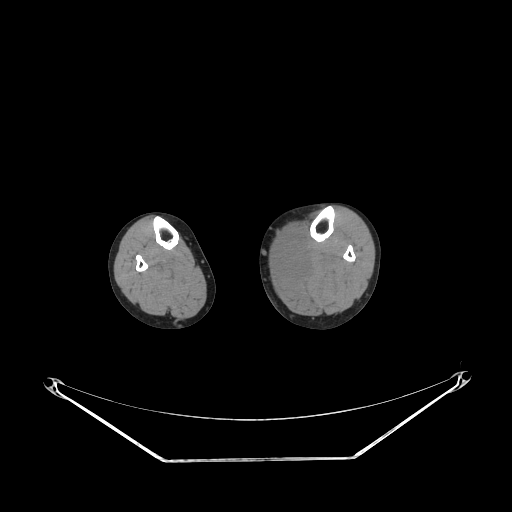
CT of an extremity soft-tissue mass (from a PET/CT study), one axial slice. Position 132 of 223 along the scan axis. Reconstruction kernel STANDARD. 140 kVp. Soft-tissue window (W 400 / L 40 HU). 3.75 mm slice thickness. 512 × 512 image matrix, field of view 500 × 500 mm. Female patient. From the clinical record (not read from this slice): histological type: extraskeletal high grade osteogenic sarcoma; grade: high; site of the primary tumour: left calf.
Annotated regions visible in this slice (expert contour drawn on MRI and transferred to this co-registered scan by the dataset authors):
- gross tumour volume (mass): box from (x=278, y=240) to (x=307, y=279) px